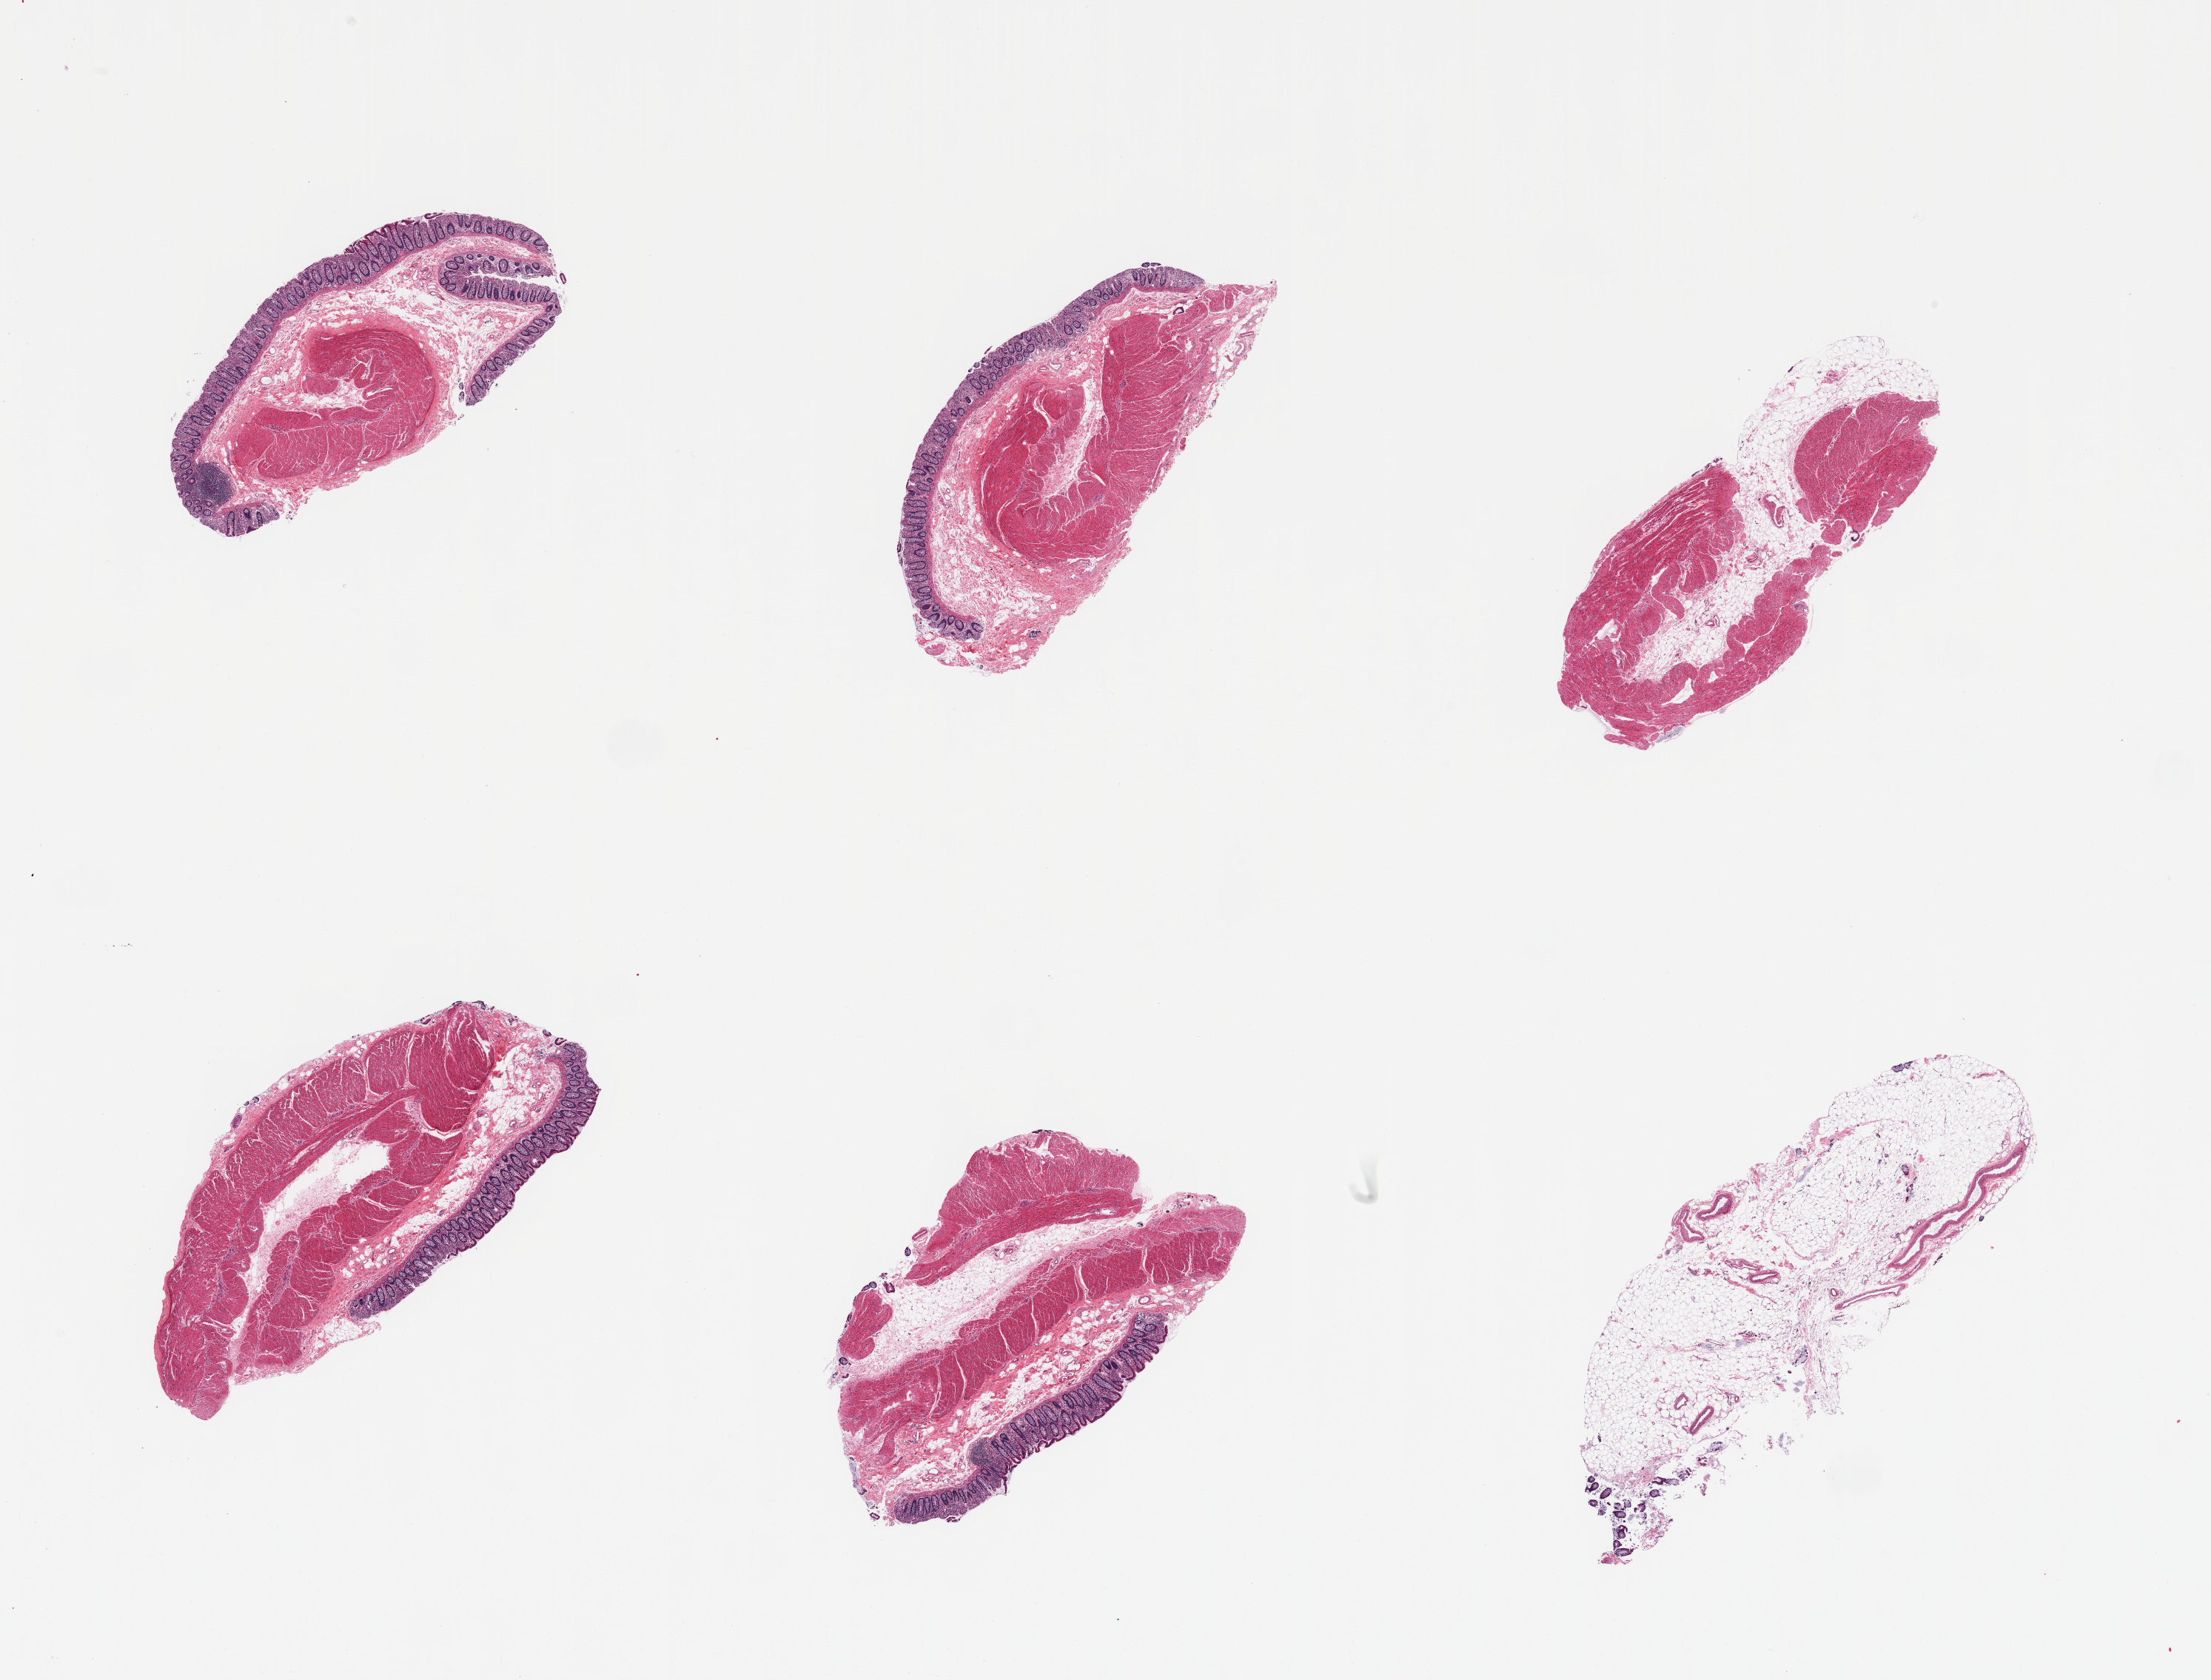
Hematoxylin and eosin (H&E) whole-slide image, shown as a low-resolution overview of the whole scanned area (about 23.6 x 18.0 mm), PAXgene-fixed, paraffin-embedded tissue, sampled site (target tissue): transverse colon, tissue donor sample. Donor sex: male.
Review note (as recorded): 6 pieces, surface mucosa moderately autolyzed, up to ~0.3mm.